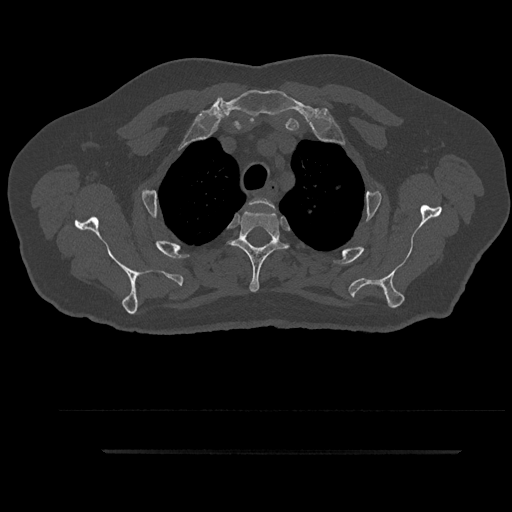
CT including the spine, one axial slice. Position 717 of 797 along the scan axis. Reconstruction kernel Br40s/3. 120 kVp. Bone window (W 1800 / L 400 HU). 0.5 mm slice thickness. 512 × 512 image matrix. Patient: male, 63 years. From the clinical record (not read from this slice): primary cancer: renal; vertebrae with lytic lesions (as recorded): T8.
Structures marked on this image (semi-automatic segmentation, software-assisted and operator-edited):
- T2 vertebra: bounding box (x1, y1, x2, y2) in pixels: (249, 198, 274, 208)
- T3 vertebra: (229, 210, 289, 292)